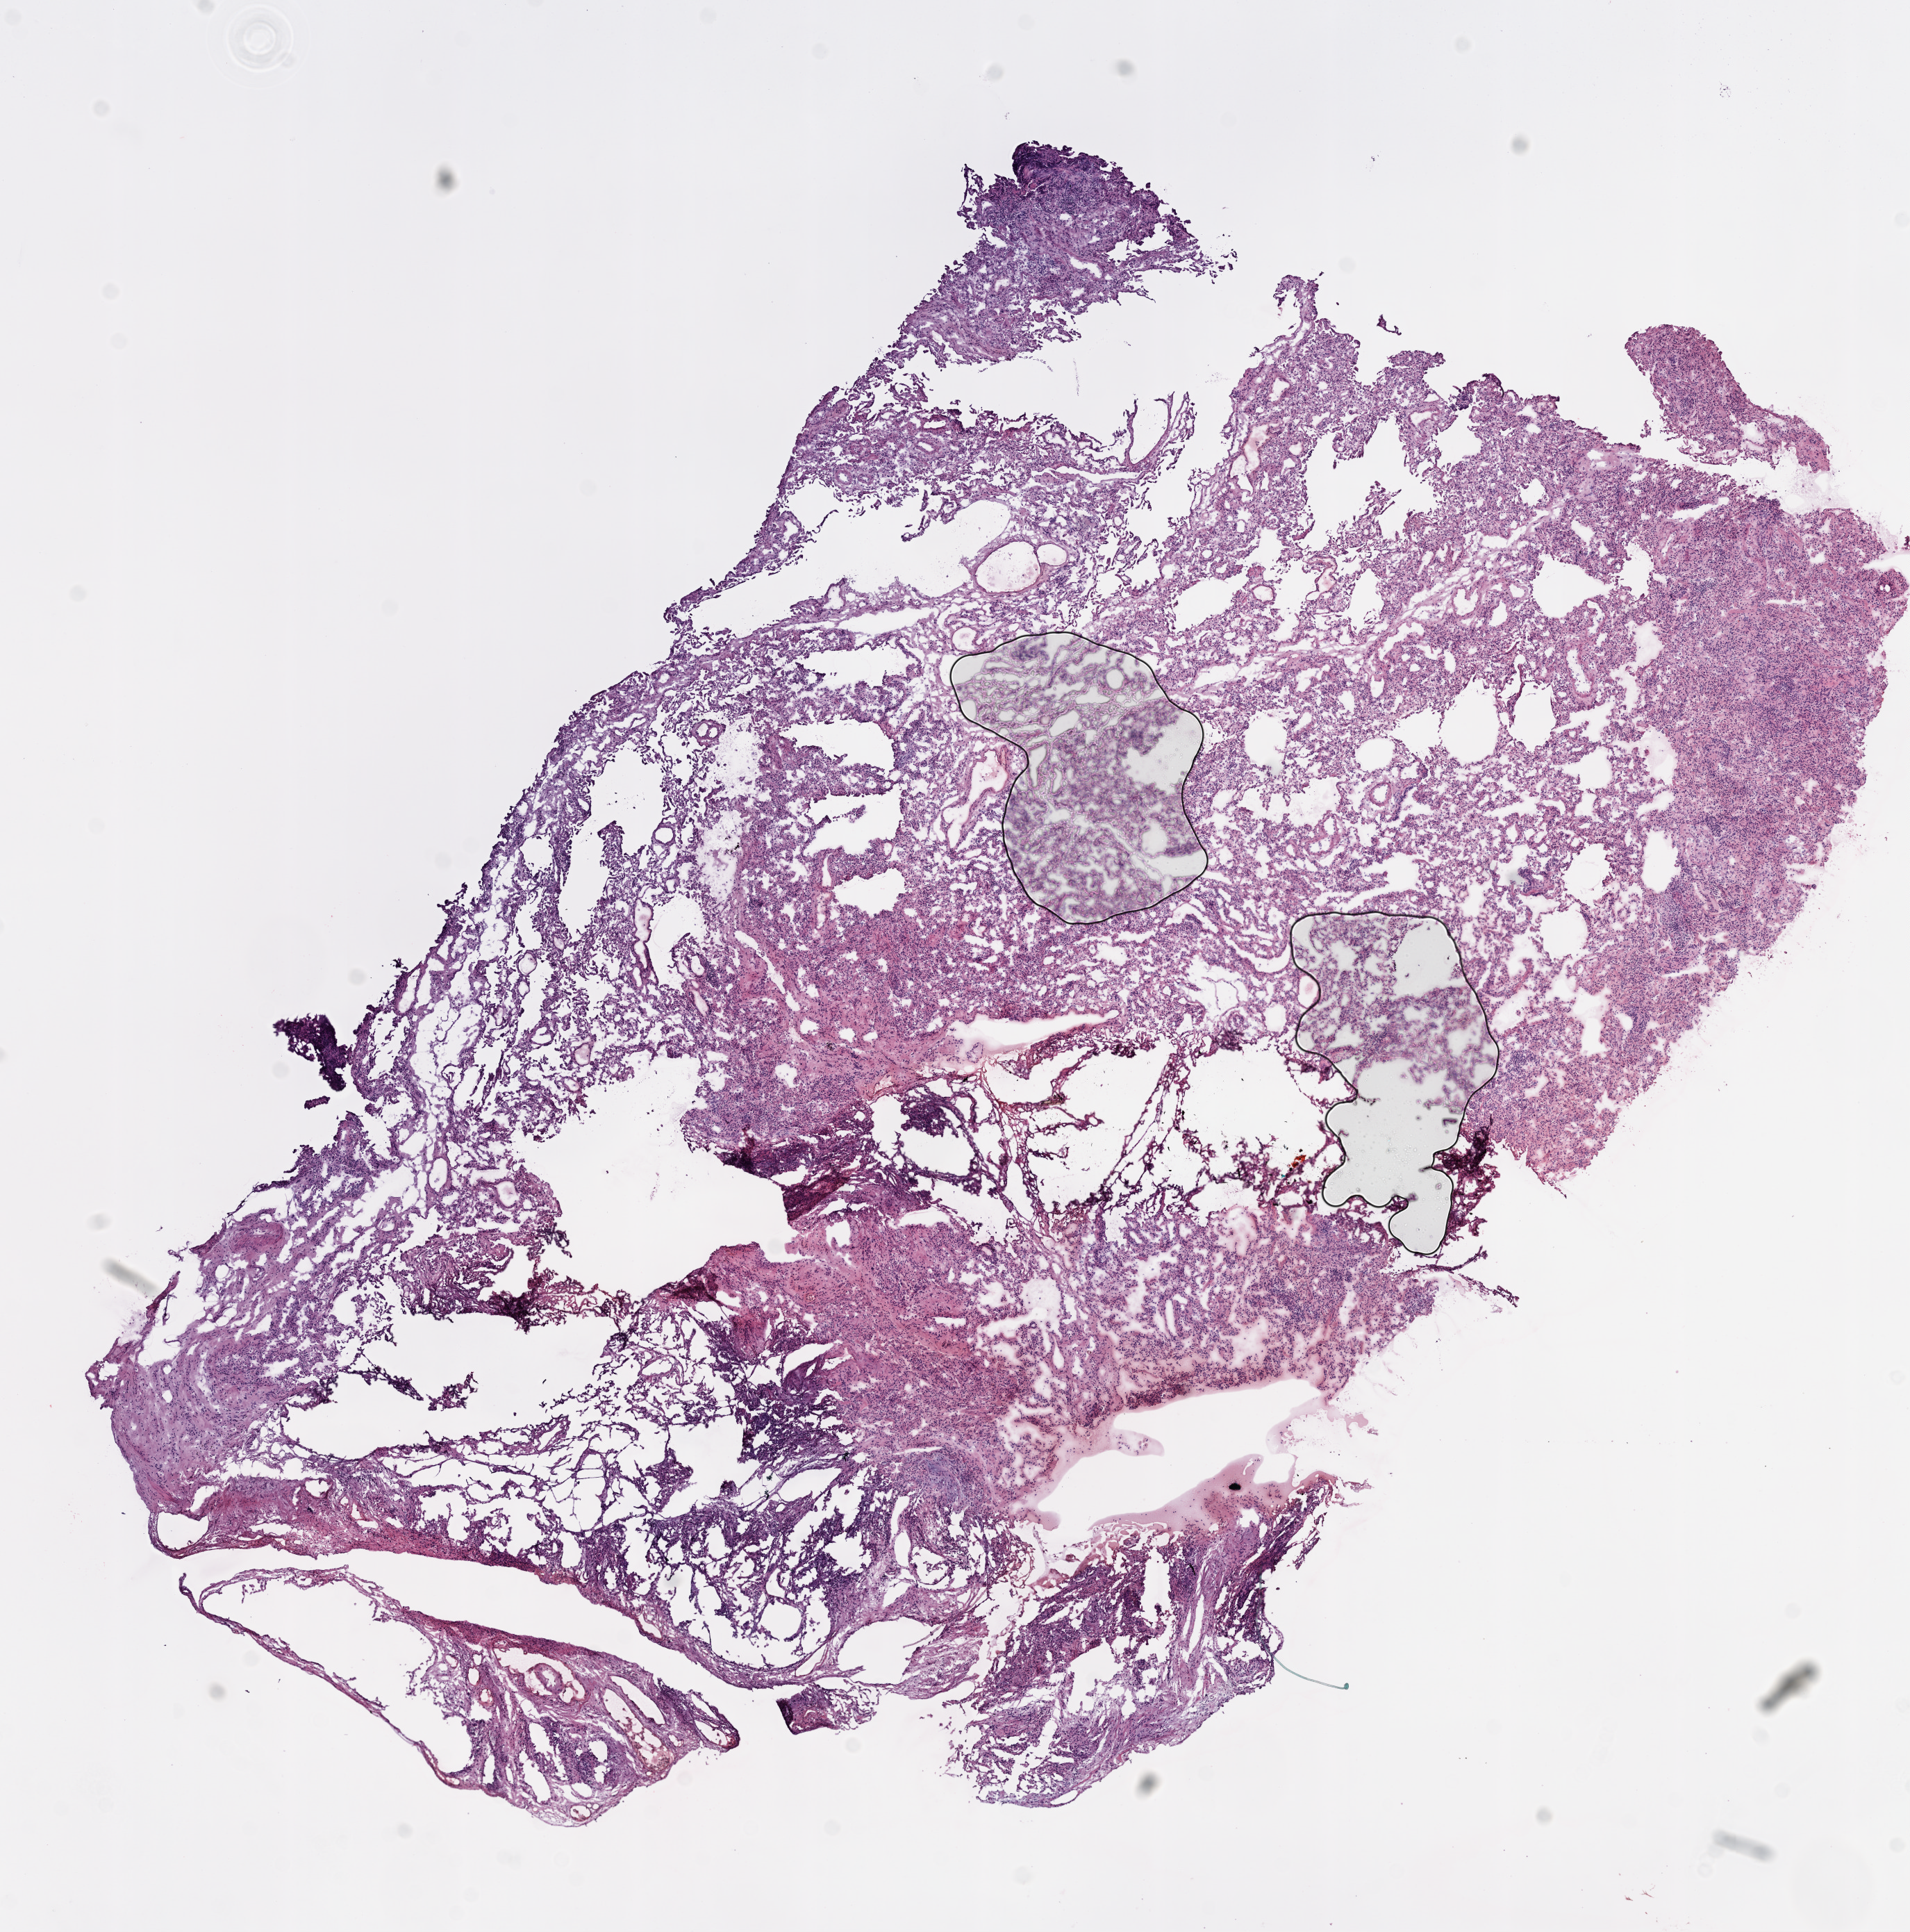
Digitized H&E tissue section (whole slide) — a low-resolution overview of the entire scanned area, about 11.0 x 11.2 mm. Frozen section. Lung, solid tissue normal (non-tumour tissue) sample. Female, age 69 years at initial diagnosis.
This section: solid tissue normal sample (biorepository sample class). Patient diagnosis: Adenocarcinoma, NOS (middle lobe, lung).